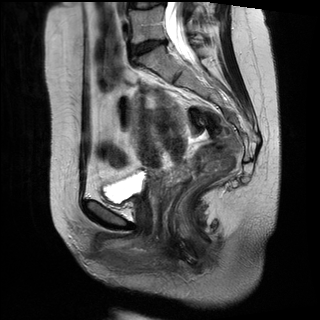
Pelvic MRI for cervical cancer, one sagittal slice. Position 16 of 34 along the scan axis. T2-weighted. 1.5 T. TE 89 ms, TR 3320 ms. 4 mm slice thickness. 320 × 320 image matrix. Female patient, age 49 years.
Outlined on this slice (expert manual segmentation):
- uterus and cervix: bounding box (x1, y1, x2, y2) in pixels: (132, 86, 193, 201)